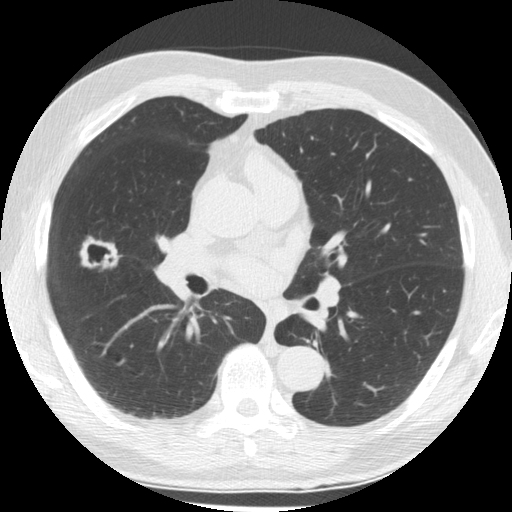
Low-dose screening chest CT, axial slice. Baseline screening round. Lung window (W 1500 / L -600 HU). 2.5 mm slice thickness. Standard (soft-tissue) reconstruction kernel (STANDARD). 512 × 512 image matrix, field of view 348 × 348 mm. Male participant, aged 64 years at enrolment. Former smoker at enrolment.
Lesion marked by an expert reader, bounding box [x1, y1, x2, y2] px = [66, 221, 129, 285]. The screening reader recorded 2 non-calcified nodules or masses ≥4 mm on this exam (right middle lobe, left lower lobe); which of them this box marks is not recorded. Official screen result: positive, change unspecified: nodule(s) >= 4 mm or enlarging nodule(s), mass(es), or other non-specific abnormalities suspicious for lung cancer. Participant outcome: lung cancer diagnosed 58 days after this screen — papillary adenocarcinoma, NOS, right middle lobe, well differentiated (G1), stage IA (AJCC 6th edition), 25 mm at pathology.